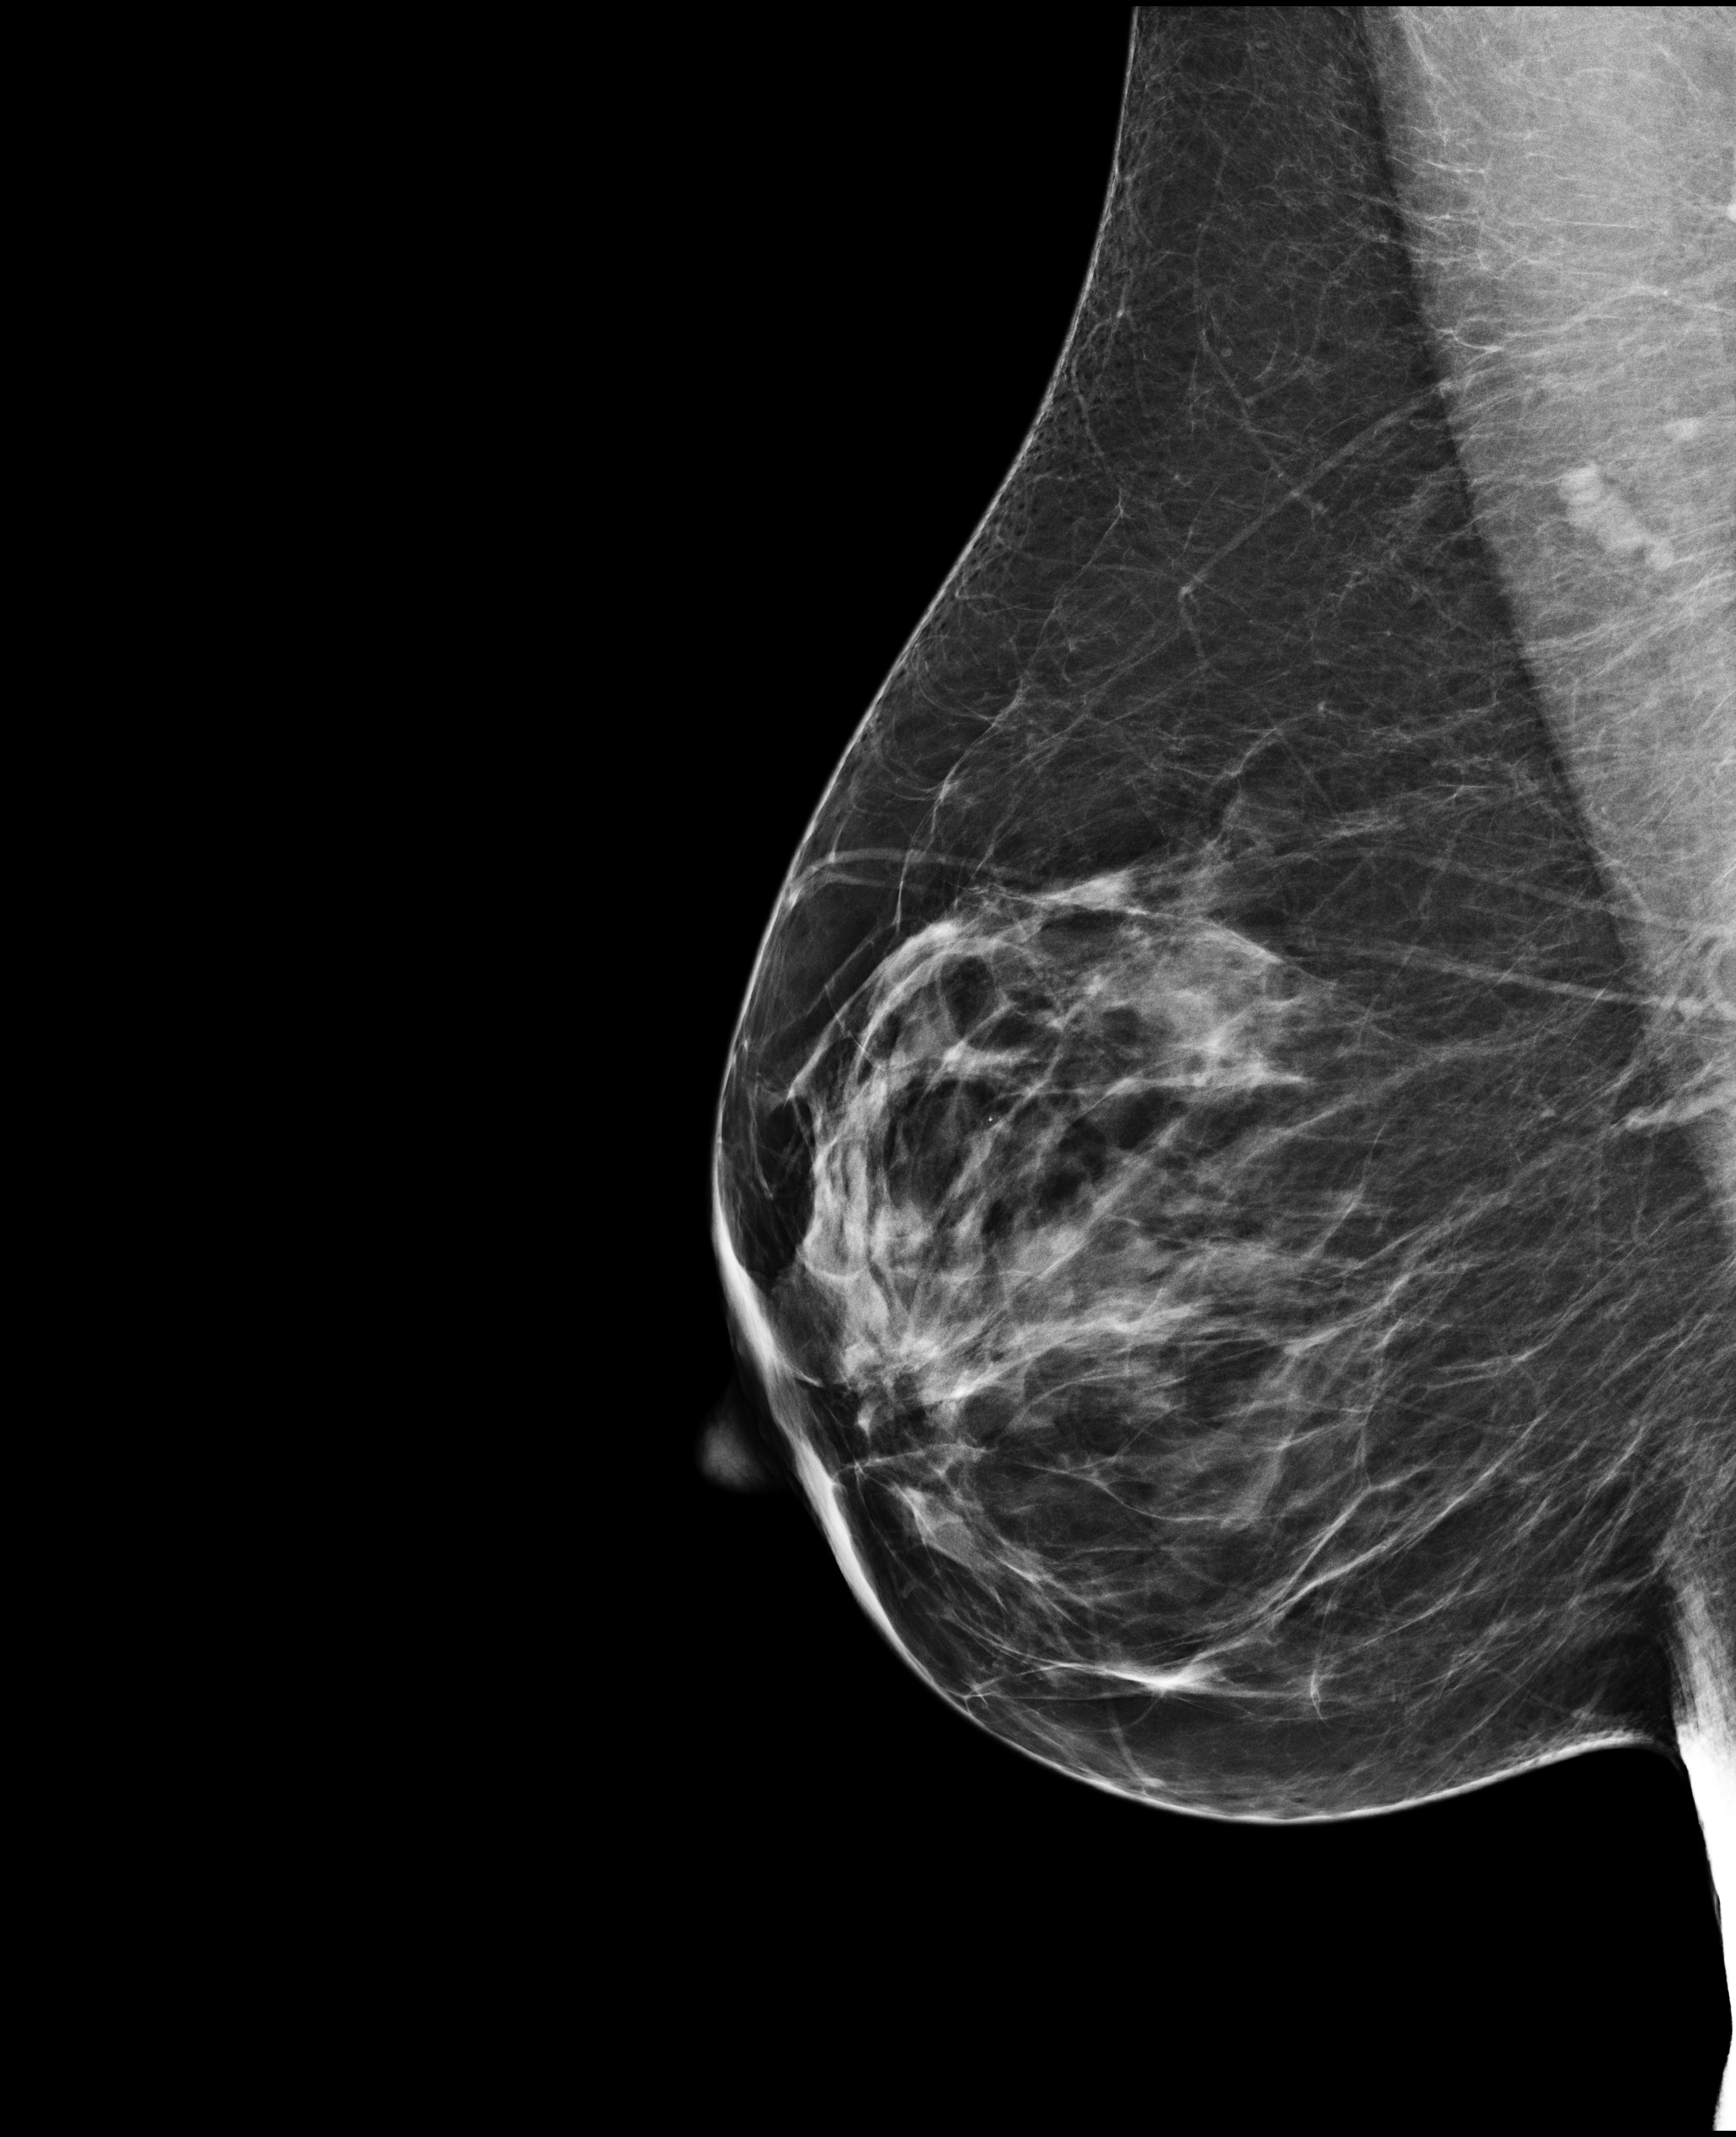
Annual screening mammography examination; compressed breast thickness 67 mm; system: Selenia Dimensions. Patient aged 57 years (female).
Image type: full-field digital mammogram. Breast: right. Projection: mediolateral oblique (MLO) view. BI-RADS breast density category at the screening exam (both breasts, scale 1–4): 3. Final BI-RADS assessment for this screening round (tomosynthesis exam, both breasts): category 1. Recall: no recall after this screen.